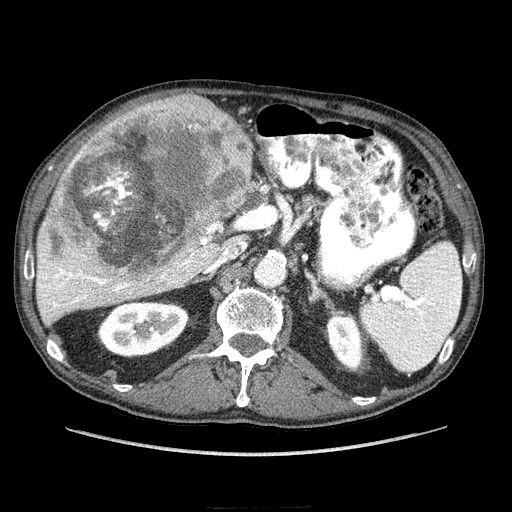
Contrast-enhanced abdominal CT (liver protocol), one axial slice; slice 139 of 218 in the series (ordered by position); reconstruction kernel STANDARD; 100 kVp; soft-tissue window (W 400 / L 40 HU); 512 × 512 image matrix, field of view 380 × 380 mm. From the clinical record (not read from this slice): diagnosis: hepatocellular carcinoma (patient treated with transarterial chemoembolisation; whether this scan precedes or follows treatment is not stated here); TNM stage (as recorded): Stage-IIIA; Child-Pugh class: A; tumour differentiation: well differentiated; tumour nodularity: multinodular.
Annotated regions visible in this slice (semi-automatic segmentation, software-assisted and operator-edited):
- liver parenchyma outside the tumour (the mass and vessels are separate outlines, so this box may not span the whole liver): box from (x=36, y=102) to (x=252, y=323) px
- mass: (x=35, y=91)–(x=253, y=280)
- liver vessels: (x=38, y=259)–(x=192, y=310)